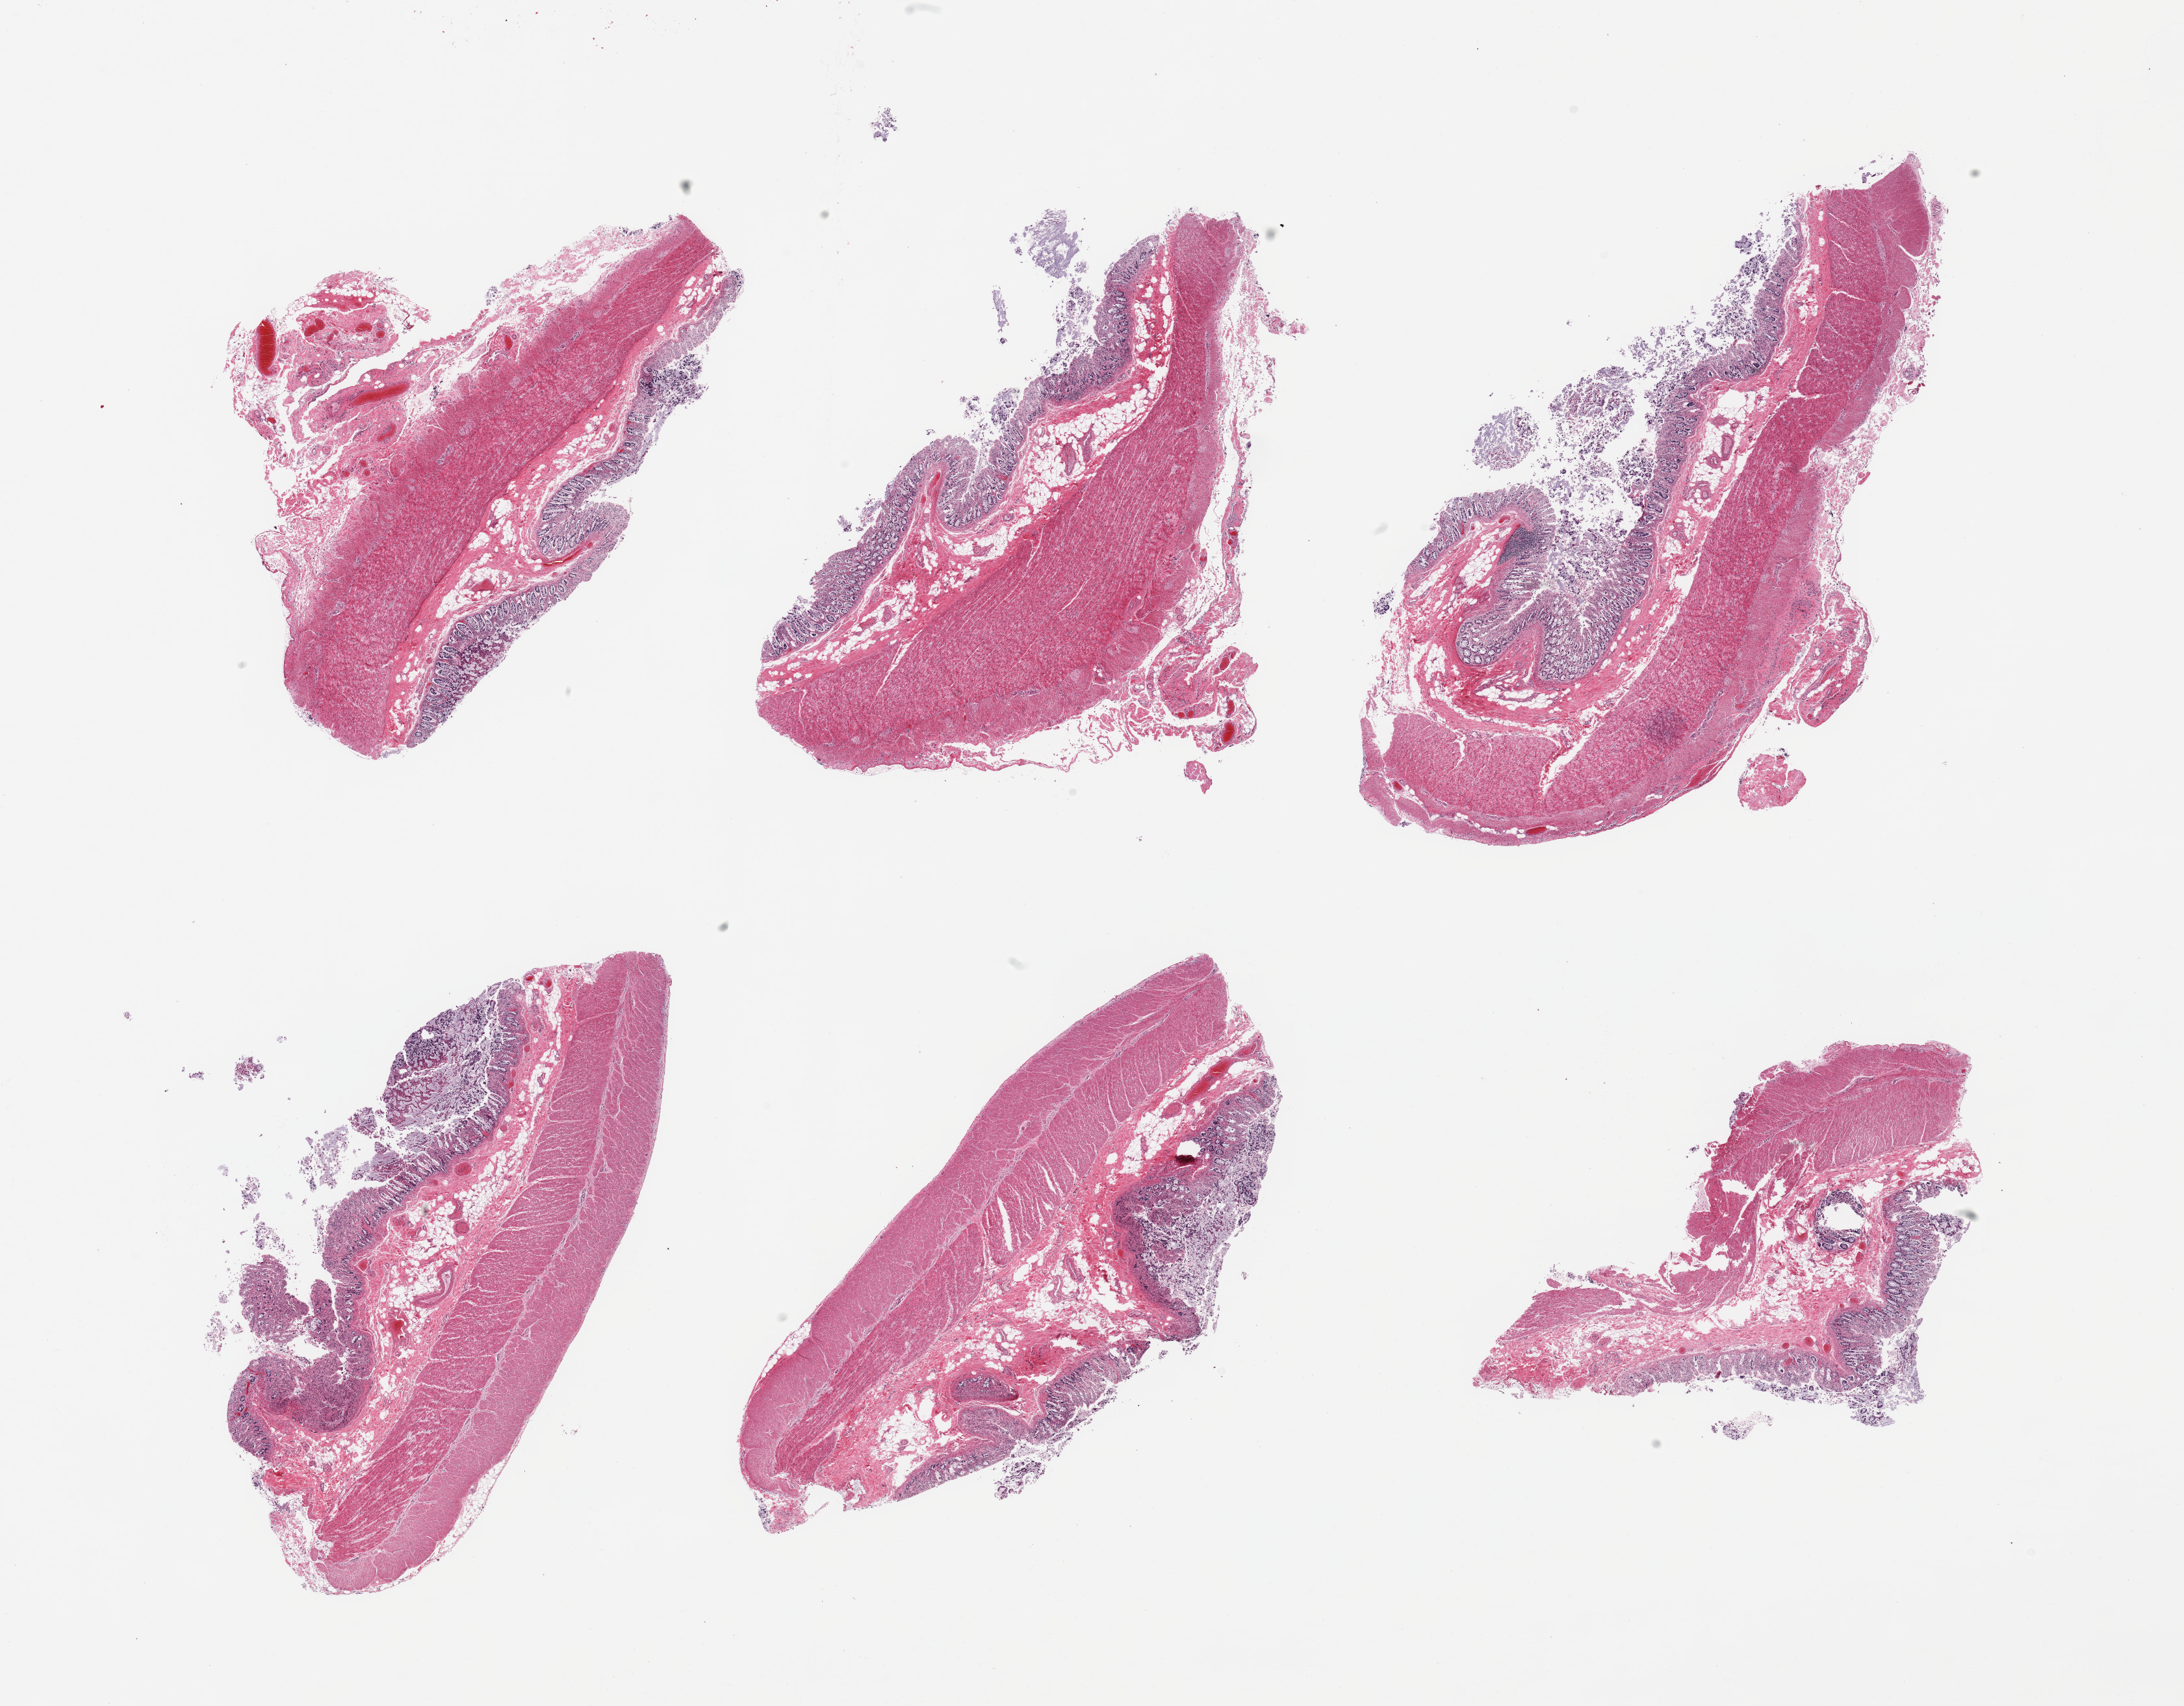
H&E whole-slide image — low-resolution overview of the scanned area, about 26.6 x 20.8 mm (acquisition: 20x scan), PAXgene-fixed paraffin-embedded (PFPE) section, section of sigmoid colon (target tissue), tissue donor sample. Donor: male.
• review note (as recorded): 6 pieces, confrimed target muscularis; contaminant autolyzed mucosa present